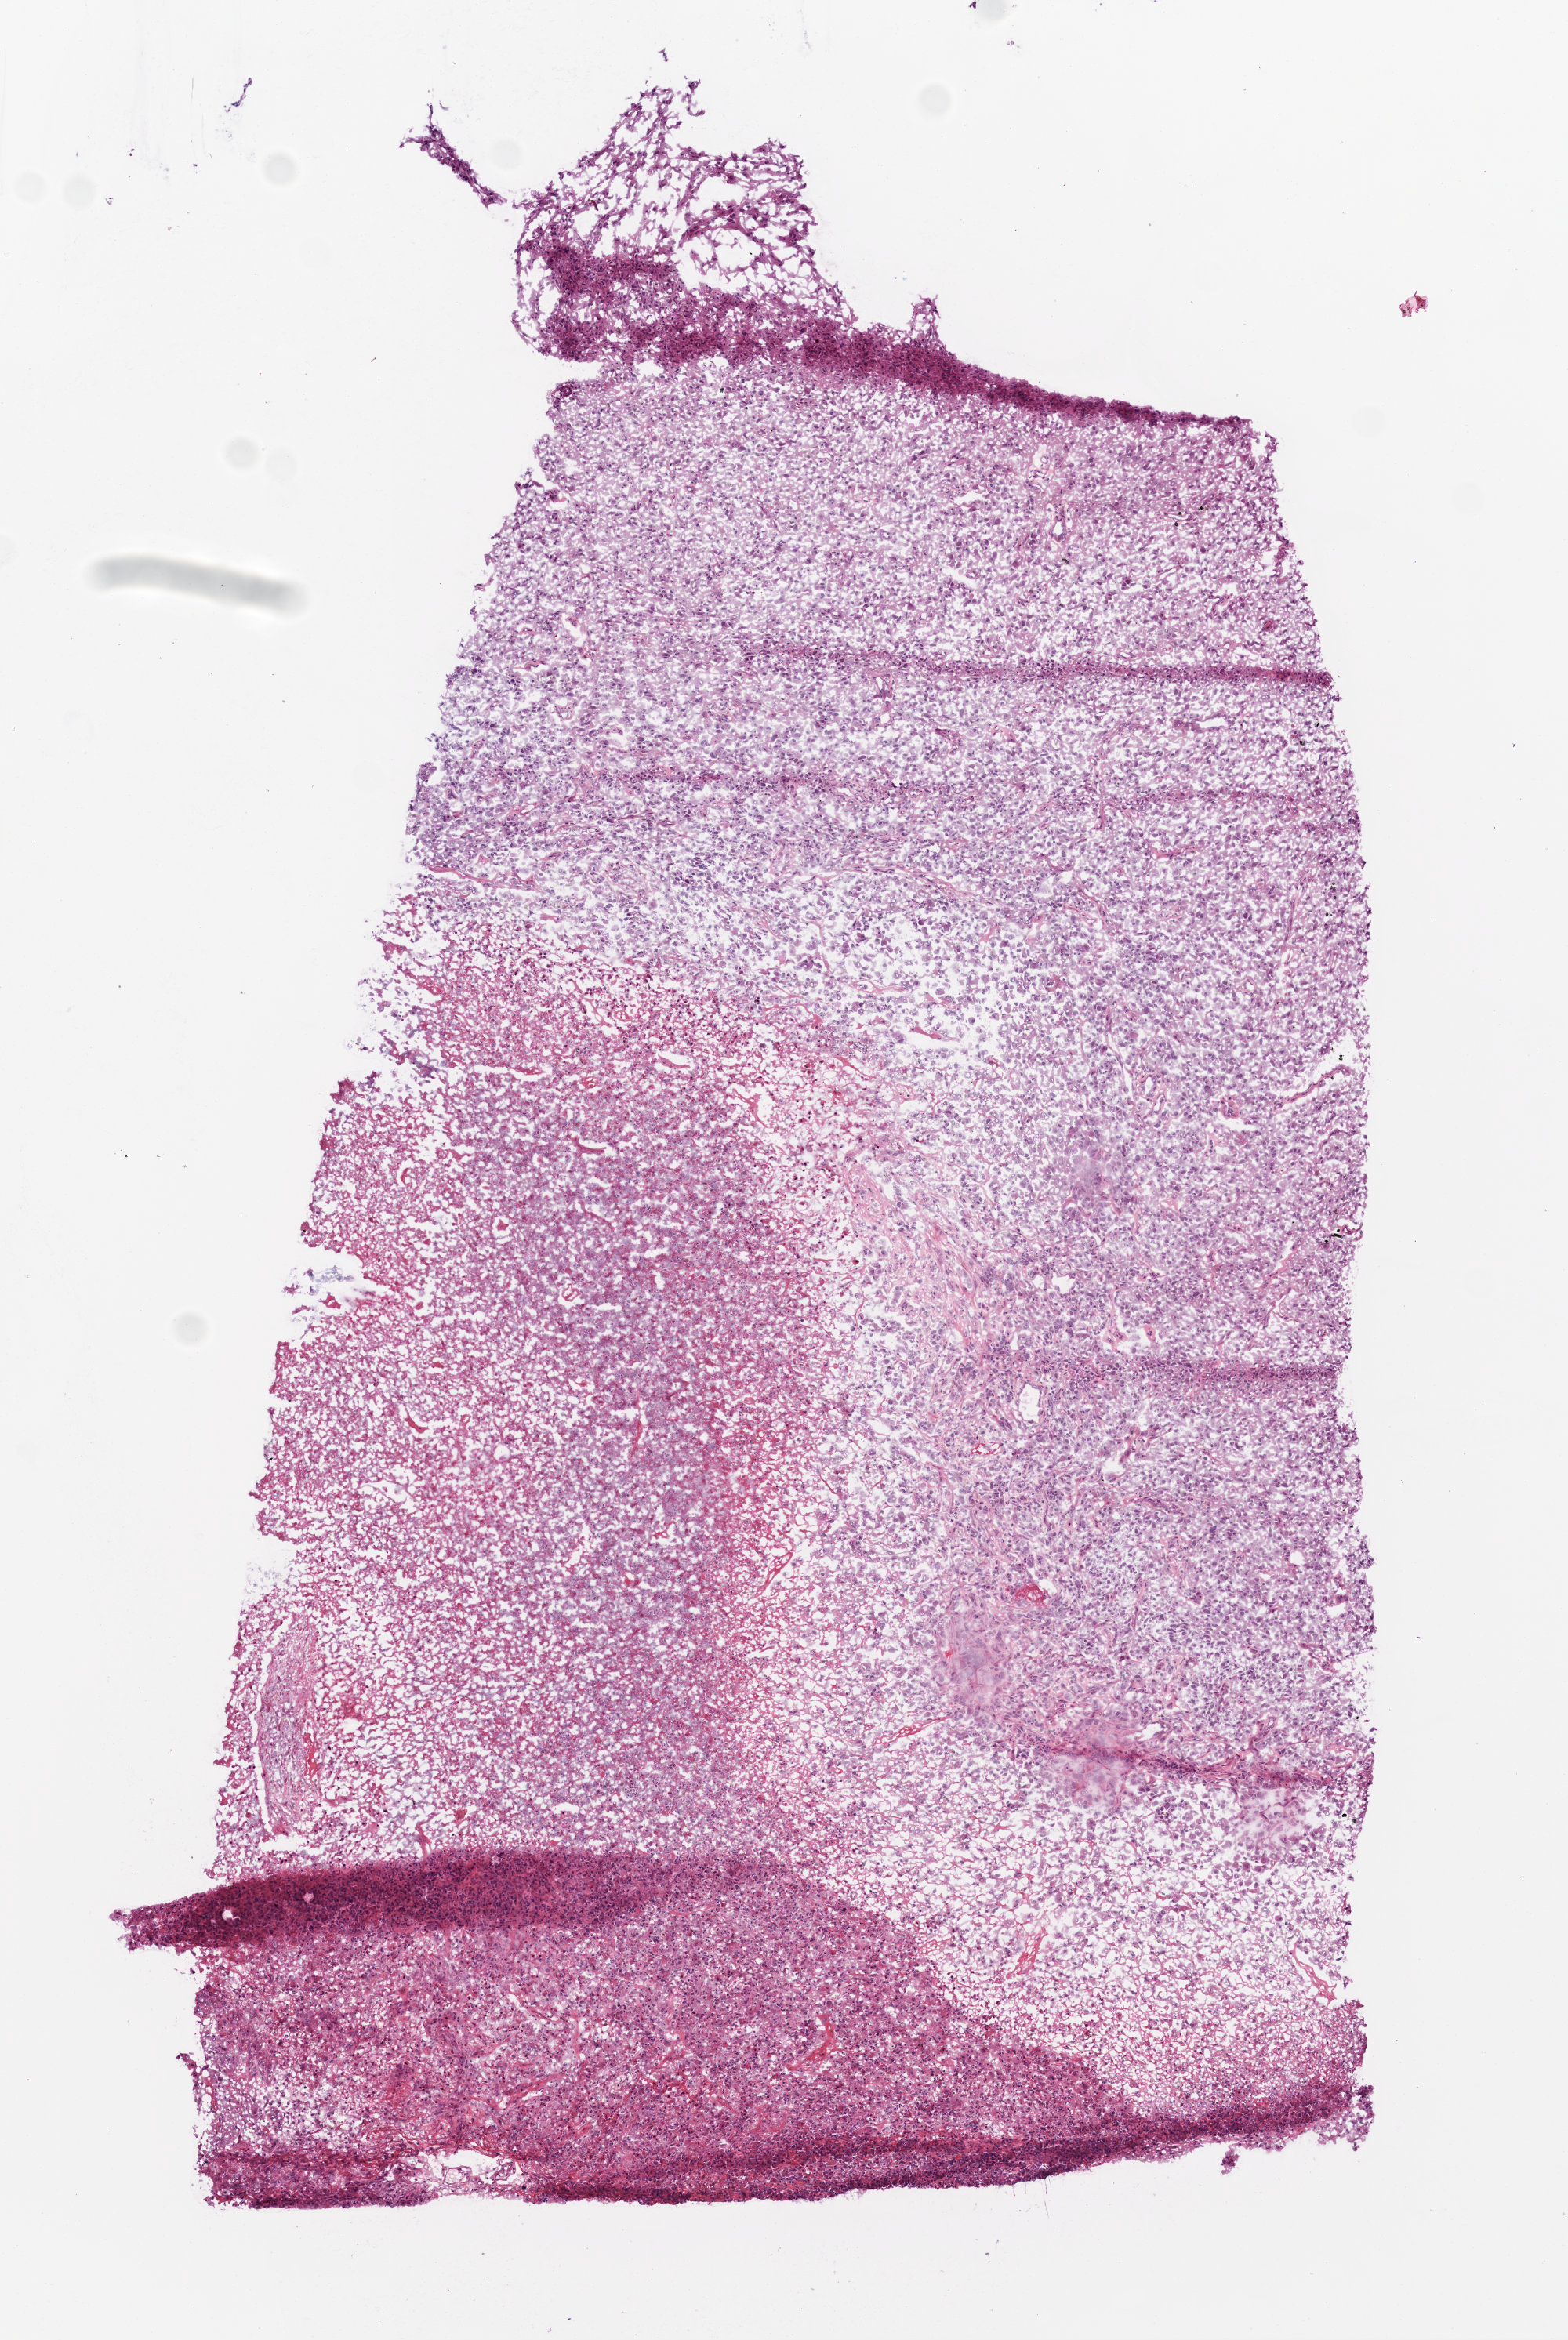
Whole-slide histology image, H&E, low-resolution overview of the scanned area, about 4.0 x 6.0 mm (from a 20x scan). Frozen section. Brain, primary tumour sample. Patient: female, age at initial diagnosis 69 years. Slide review estimates, as recorded: tumour cells 80%, tumour nuclei 80%, normal cells 0%, stromal cells 0%, necrosis 20%.
Histologic diagnosis: Glioblastoma.